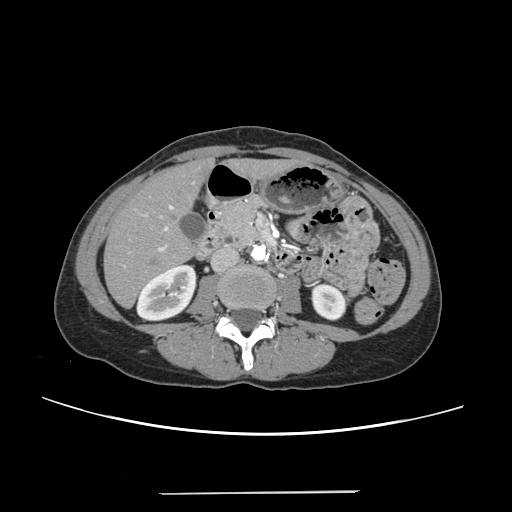
Contrast-enhanced abdominal CT, one axial slice. Slice 89 of 240 in the series (ordered by position). 120 kVp. Intravenous contrast given. Soft-tissue window (W 400 / L 40 HU). 1.25 mm slice thickness. 512 × 512 image matrix. Female patient, age 60 years. From the clinical record (not read from this slice): diagnosis: colorectal cancer liver metastases, imaged before liver resection; multiple liver metastases: no; largest metastasis: 1.5 cm.
Structures marked on this image (outlined manually by an expert reader):
- liver: bounding box <105,161,286,306> (left, top, right, bottom; pixels)
- planned liver remnant (the part of the liver to remain after resection): <105,163,285,305>
- portal vein (with intrahepatic branches): <123,205,173,267>